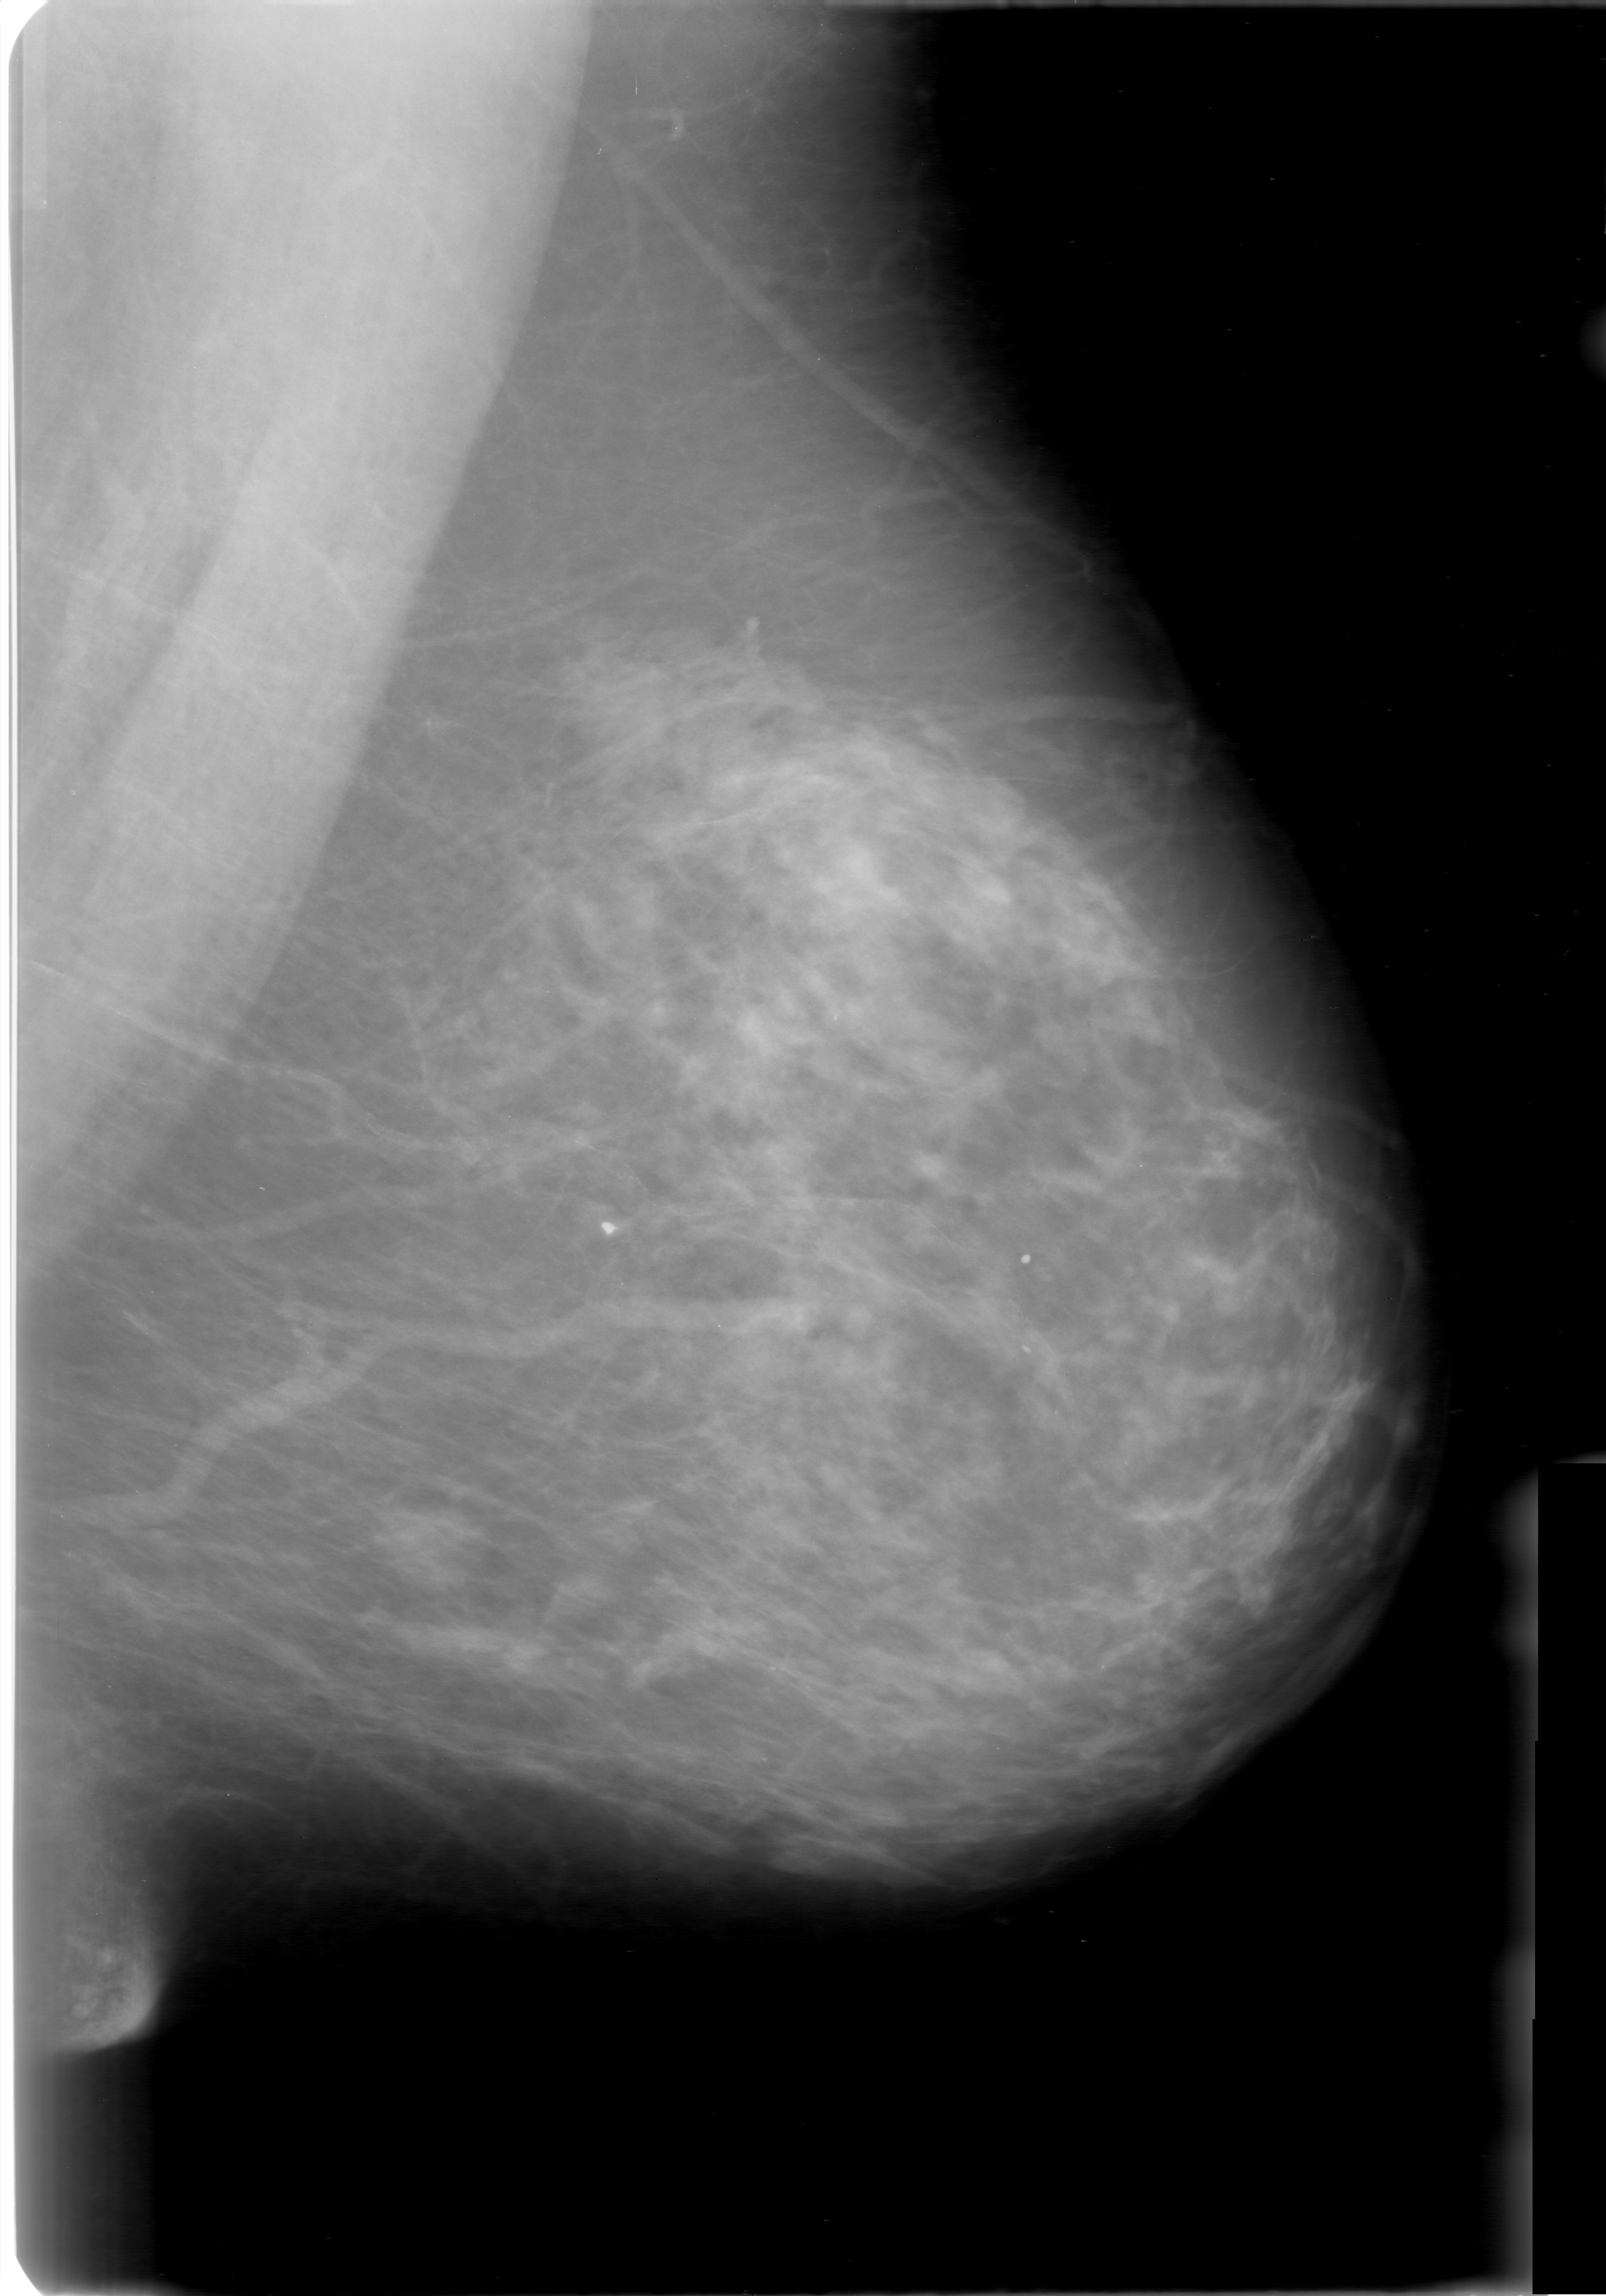
Mammogram (digitized film), left breast, mediolateral oblique (MLO) view, breast composition: heterogeneously dense (BI-RADS density category 3 of 4).
Abnormality record for this image: mass, shape lobulated, margins obscured; BI-RADS assessment category 0 (incomplete: needs additional imaging); pathology result (as recorded, not read from the image): benign.